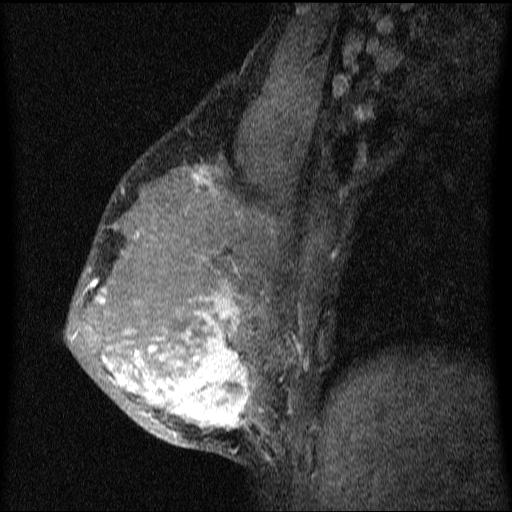
Breast MRI (dynamic contrast-enhanced), one sagittal slice. Slice 43 of 64 in the series (ordered by position). Dynamic contrast-enhanced series, image 2 of 4 at this slice position (ordered by acquisition). 1.5 T. TE 4.2 ms, TR 9.1 ms. 2 mm slice thickness. 512 × 512 image matrix. Female patient, age 33 years.
Outlined on this slice (semi-automatic segmentation, software-assisted and operator-edited):
- analysis volume of interest (the breast-tissue region the enhancement analysis was run in; not a lesion): box from (x=66, y=151) to (x=336, y=458) px
- tumour enhancement mask (voxels above the 70 % enhancement threshold inside the analysis volume of interest): (x=68, y=167)–(x=301, y=438)